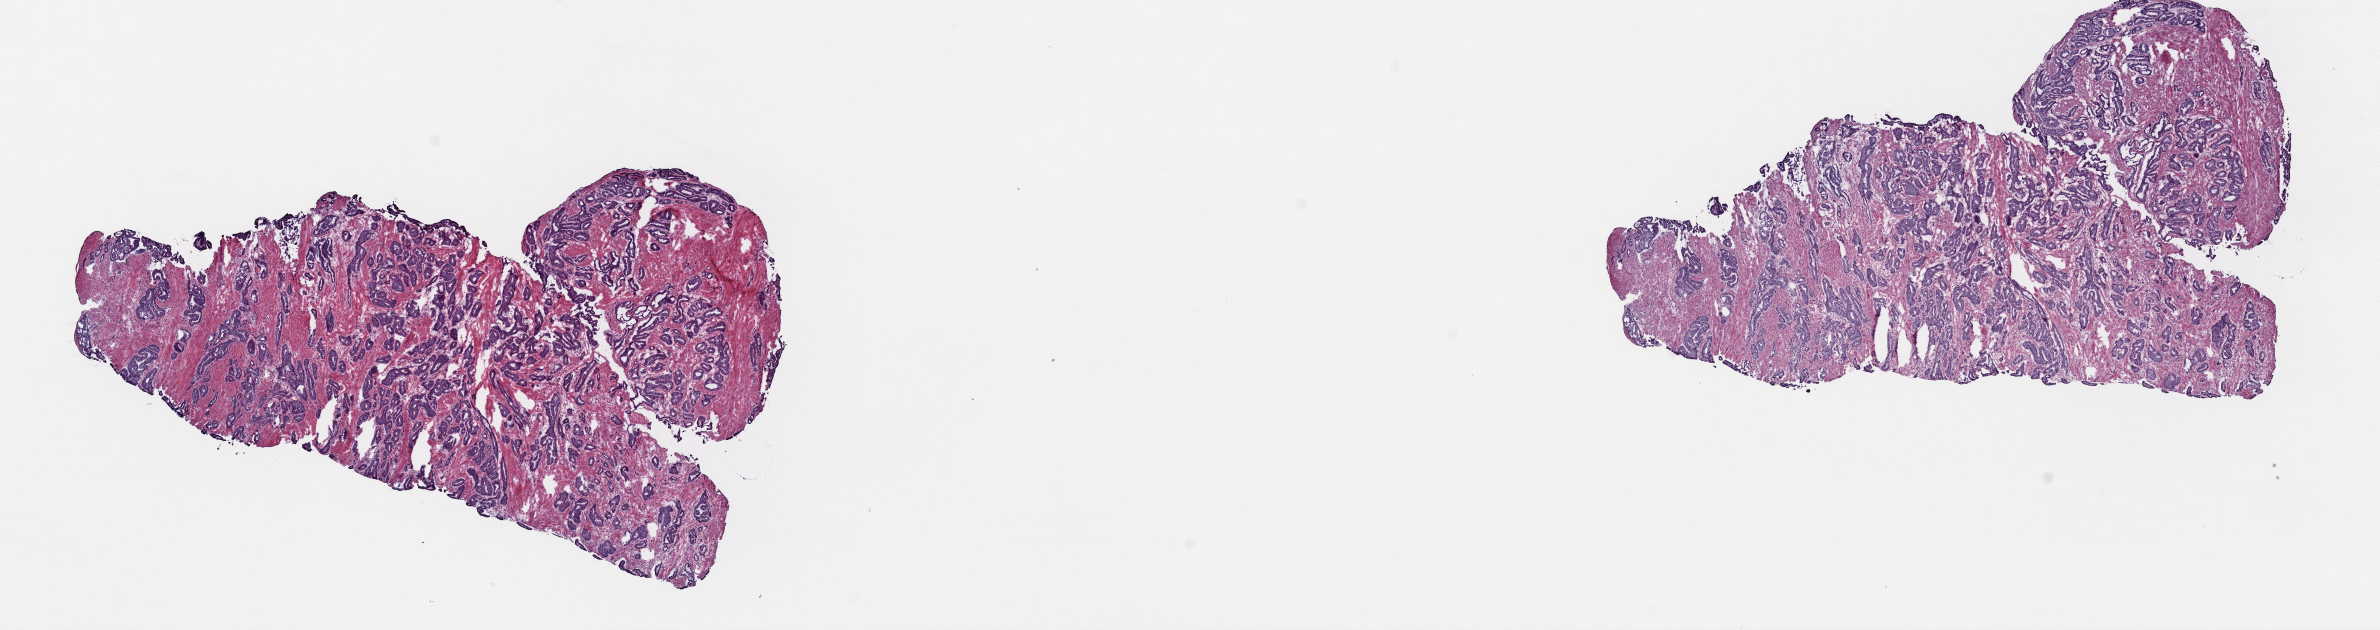
Whole-slide histology image, H&E-stained — whole scanned area (about 18.8 x 5.0 mm, slide scanned at 40x) shown as a low-resolution overview, frozen section from the top of the tissue portion, prostate, primary tumour sample. Male patient; age at initial diagnosis 63 years. Gleason score: 7 (3+4). Composition of this section per pathologist review: tumour cells 55%, tumour nuclei 75%, normal cells 0%, stromal cells 45%, necrosis 0%. Infiltration values recorded for this section: lymphocyte infiltration 4%, monocyte infiltration 0%, neutrophil infiltration 0%.
Lymph nodes positive (case pathology): 0 of 19 examined. Diagnosis: Adenocarcinoma, NOS (prostate gland).